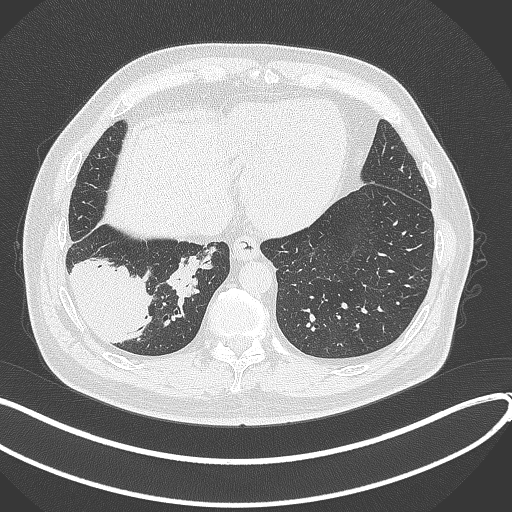
Chest CT, one axial slice. Slice 84 of 360 in the series (ordered by position). 120 kVp. Lung window (W 1500 / L -600 HU). 1 mm slice thickness. 512 × 512 image matrix, field of view 400 × 400 mm. Patient: male, 59 years.
Structures marked on this image (rectangle marked by the reading radiologist):
- lung tumour (recorded histology: adenocarcinoma): bounding box <68,253,156,349> (left, top, right, bottom; pixels)